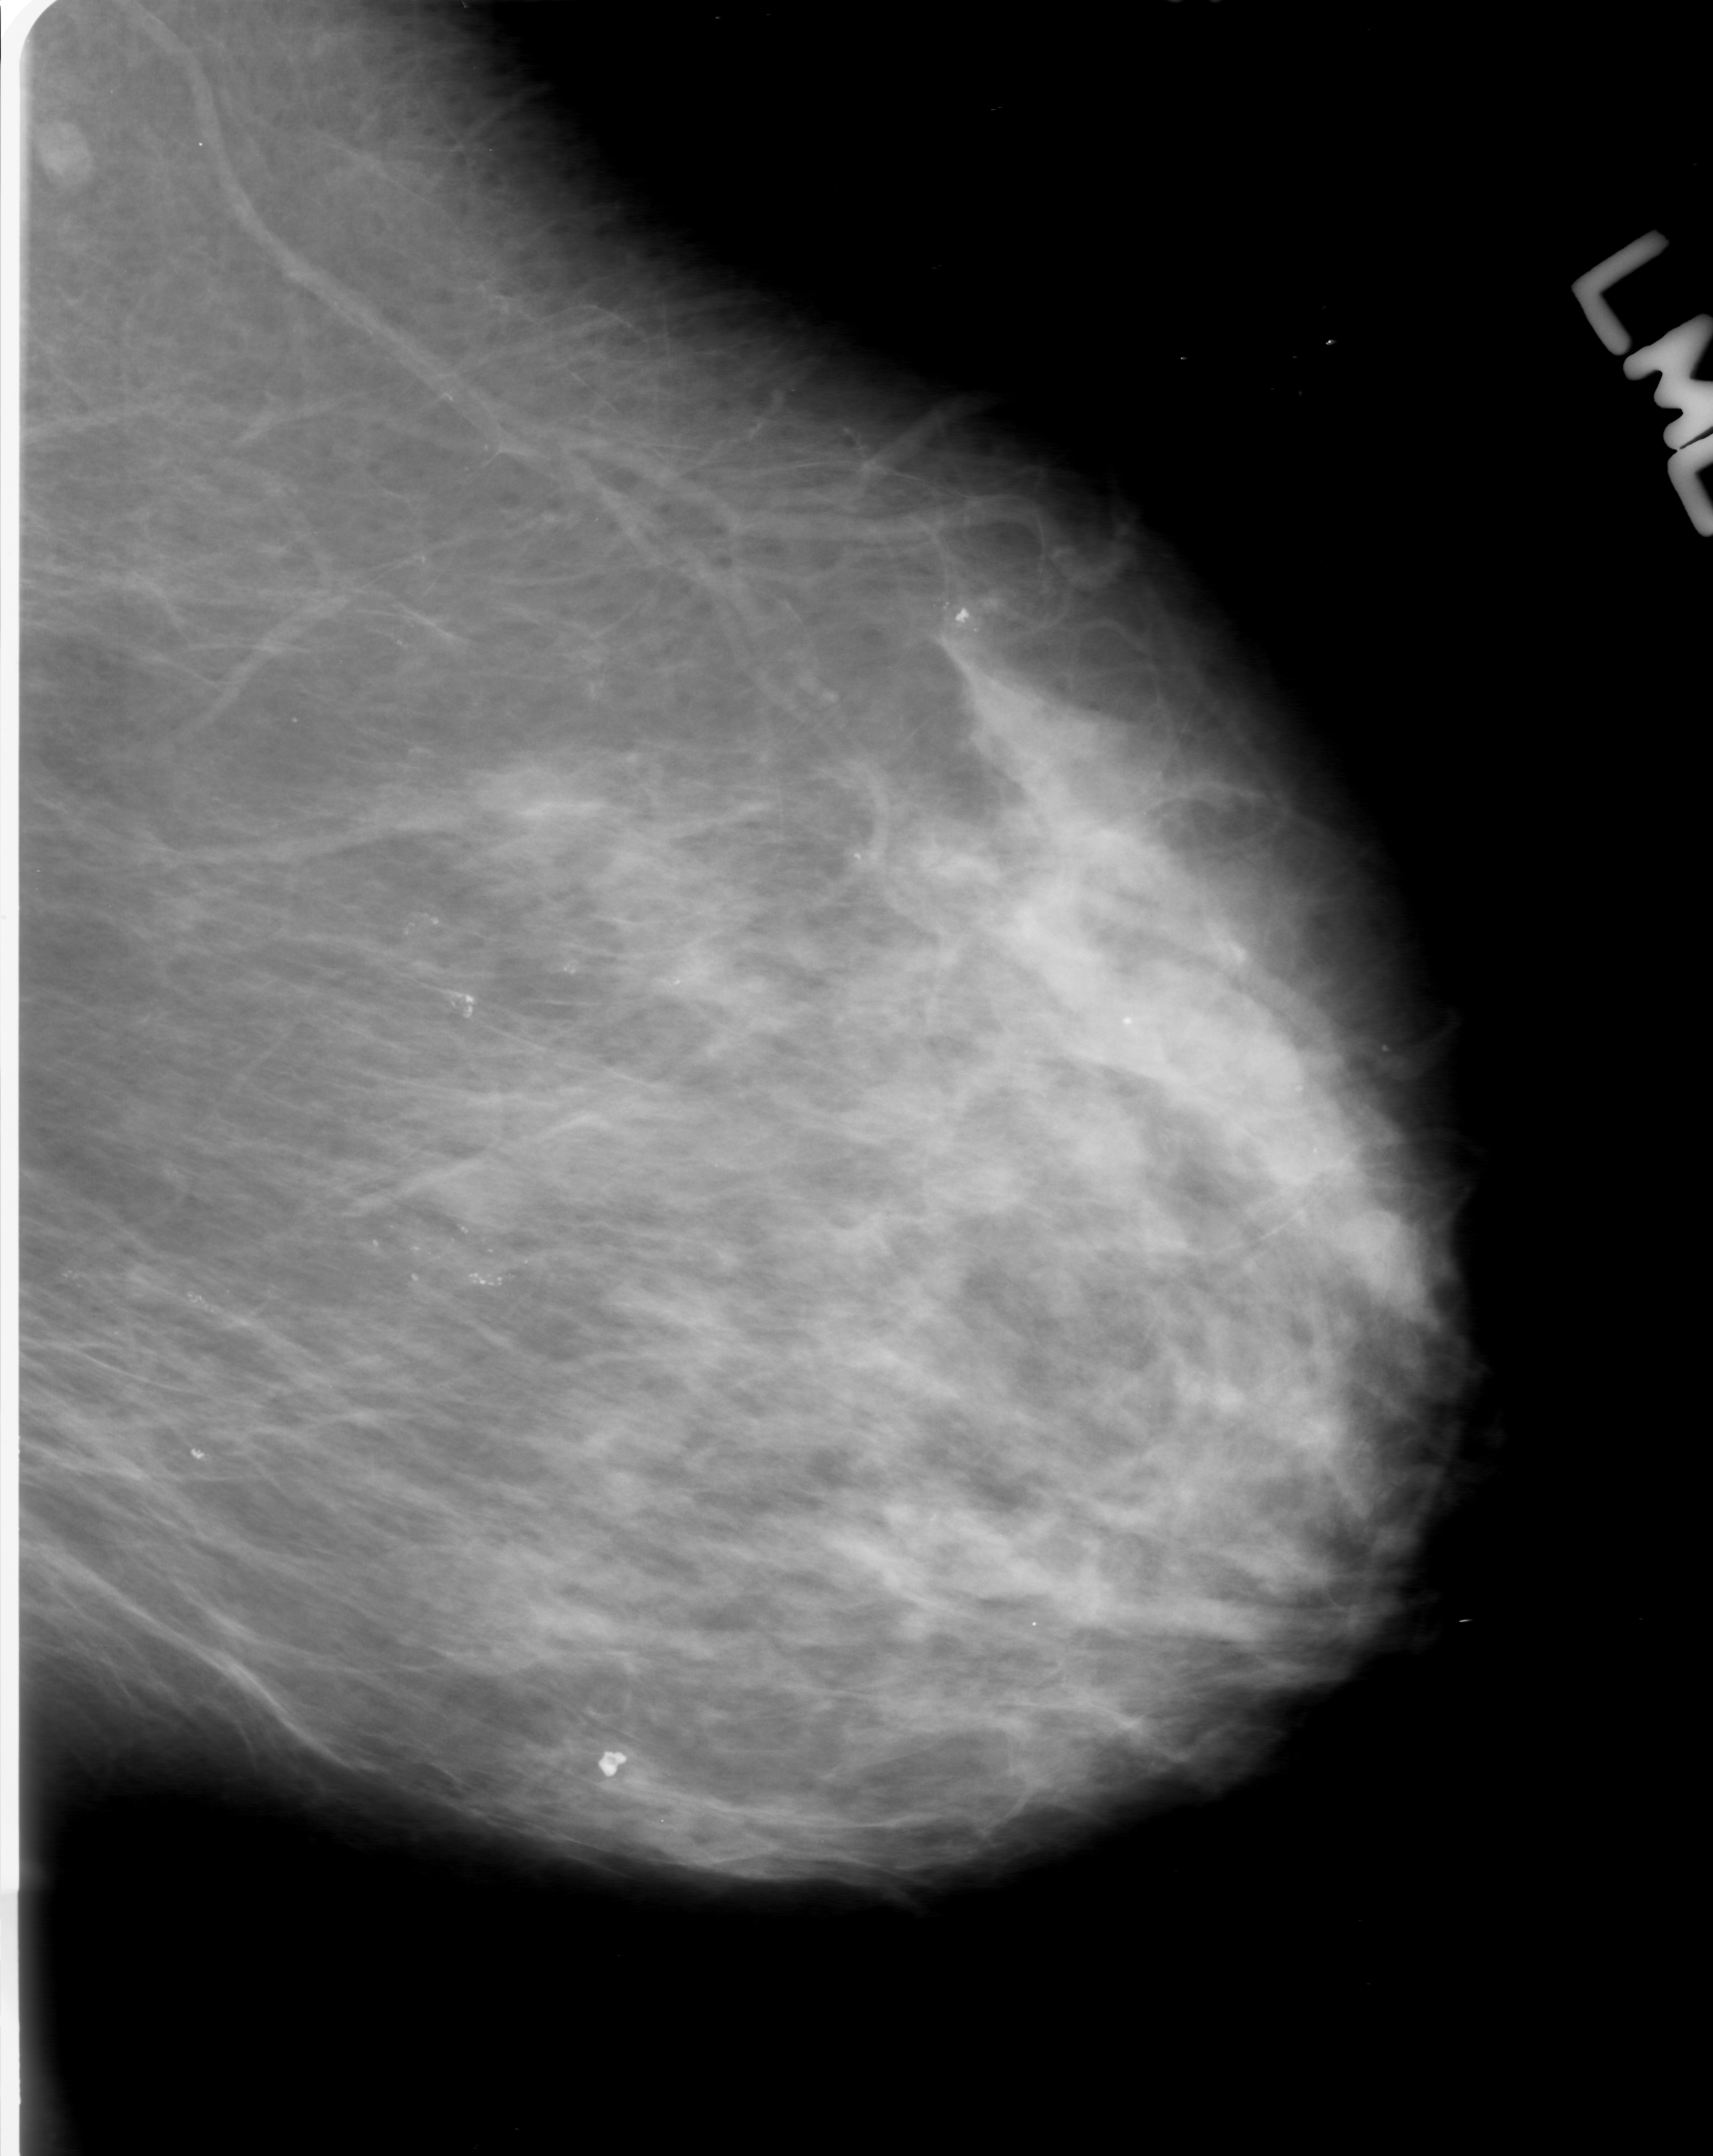
Mammogram (digitized film); left breast; MLO view; BI-RADS breast density category 2 (scale 1–4); 1713 × 2156 image matrix.
Expert-marked regions of interest on this film, with their recorded descriptors:
- calcifications, morphology round and regular / pleomorphic, distribution clustered; BI-RADS assessment category 0 (incomplete: needs additional imaging); subtlety rating 4 on a 1 (subtle) to 5 (obvious) scale; pathology result (as recorded, not read from the image): benign: bounding box <277,1147,622,1384> (left, top, right, bottom; pixels)